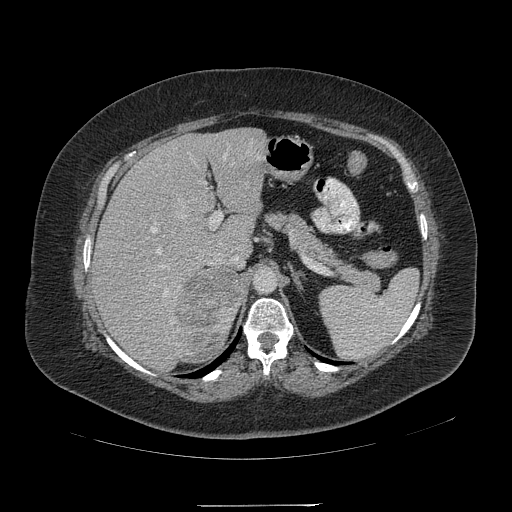
Contrast-enhanced abdominal CT, one axial slice; position 142 of 217 along the scan axis; reconstruction kernel STANDARD; intravenous contrast given; soft-tissue window (W 400 / L 40 HU); 1.25 mm slice thickness; 512 × 512 image matrix. Patient: female, 55 years. From the clinical record (not read from this slice): diagnosis: adrenocortical carcinoma; tumour side: right adrenal; tumour size at pathology: 11 cm; Ki-67 index: 20 %; stage (as recorded): 2.
Structures marked on this image (semi-automatically segmented with operator editing):
- mass: bounding box (x1, y1, x2, y2) in pixels: (176, 268, 243, 358)